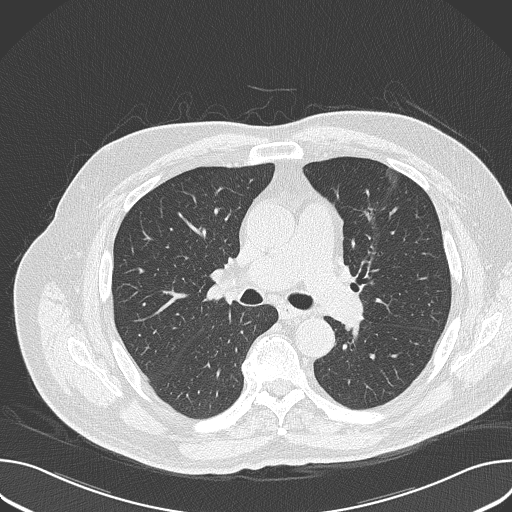
Chest CT (low-dose screening protocol), one axial image, baseline screening round, lung window (W 1500 / L -600 HU), lung (sharp) reconstruction kernel (B50f), 120 kVp, slice 69 of 168 in the series, 512 × 512 image matrix, field of view 380 × 380 mm. Male participant, aged 74 years at enrolment. Former smoker at enrolment.
- Expert reader's lesion annotation, bounding box (x1, y1, x2, y2) in pixels: (347, 200, 393, 239).
- The screening reader recorded 2 non-calcified nodules or masses ≥4 mm on this exam; which of them this box marks is not recorded.
- Official screen result: positive, change unspecified: nodule(s) >= 4 mm or enlarging nodule(s), mass(es), or other non-specific abnormalities suspicious for lung cancer.